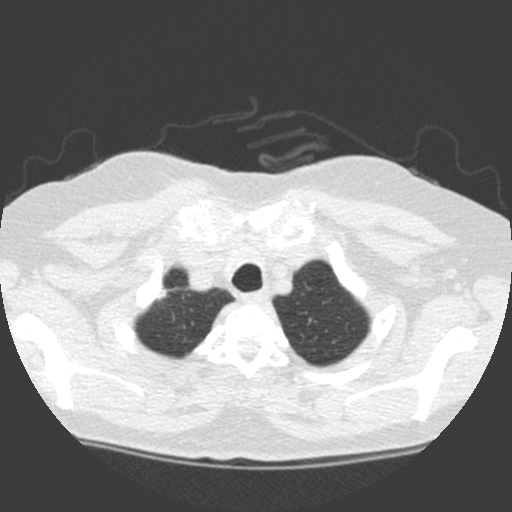
Low-dose screening chest CT, axial slice. Baseline annual screen. Lung window (W 1500 / L -600 HU). 2 mm slice thickness. Female participant, aged 63 years at enrolment. Current smoker at enrolment.
Expert-annotated lung lesion, bounding box (x1, y1, x2, y2) in pixels: (141, 278, 181, 311). The exam's reader record, not a measurement of the box and not confirmed to be the same lesion: non-calcified nodule or mass ≥4 mm, right upper lobe, 11 × 11 mm, spiculated (stellate) margins, soft tissue attenuation. Later outcome: lung cancer diagnosed 6 days after this screen — adenocarcinoma, NOS, right upper lobe, poorly differentiated (G3), stage IA (AJCC 6th edition), 17 mm at pathology.